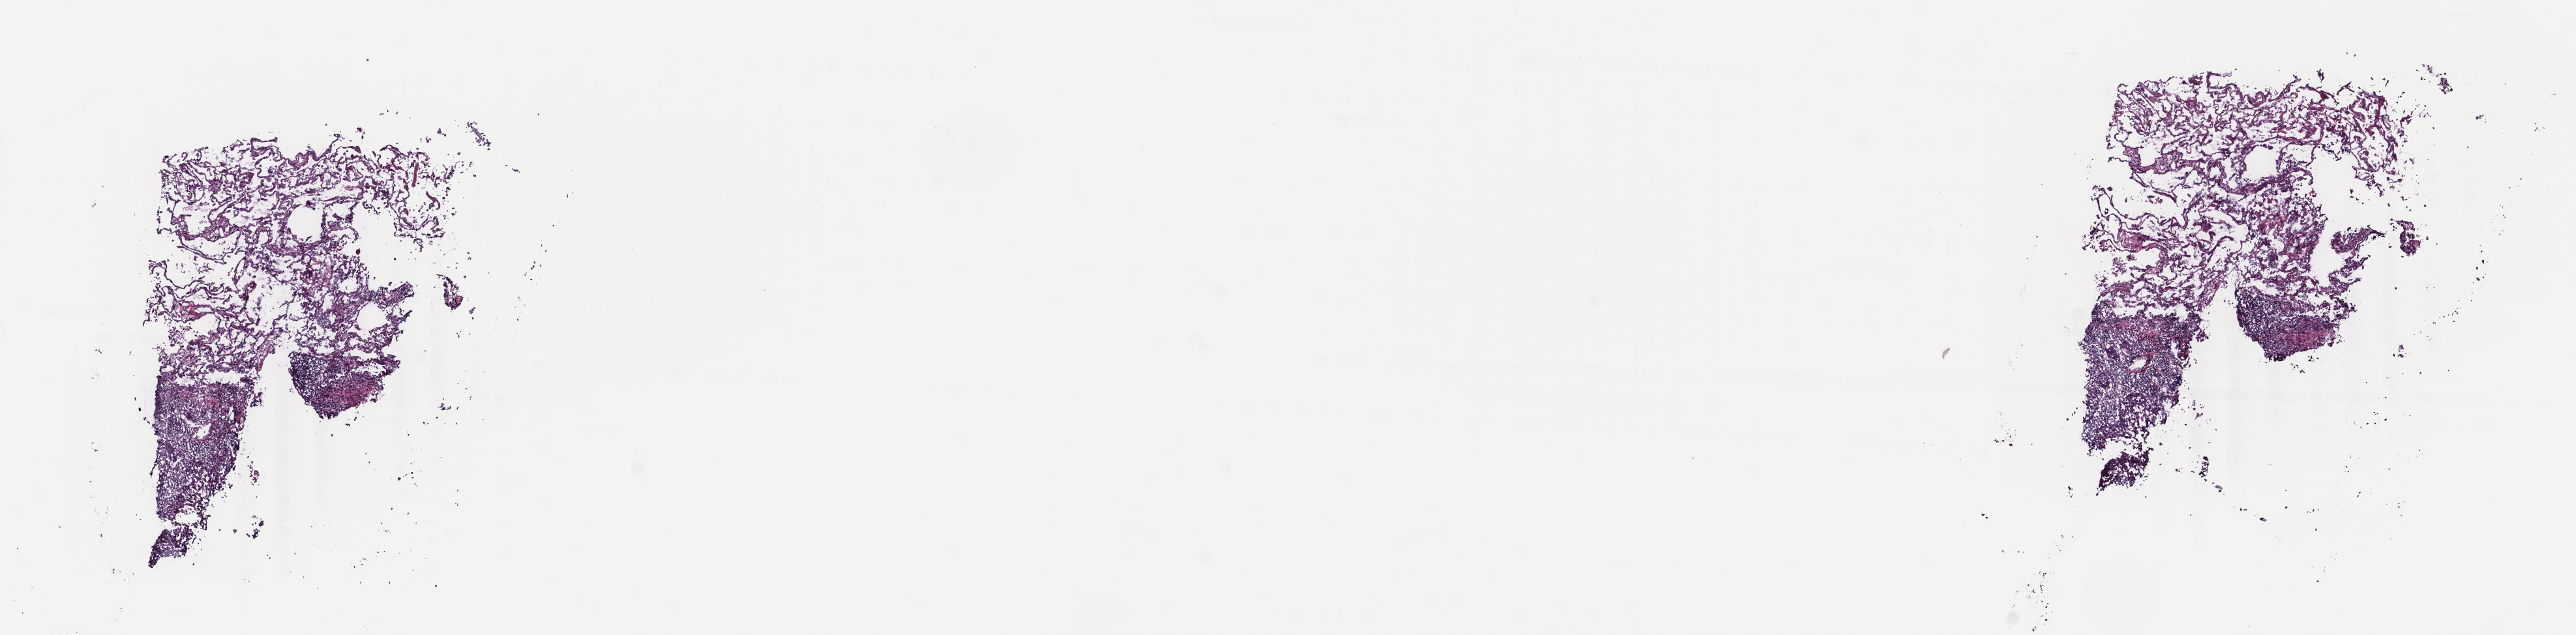
Hematoxylin and eosin (H&E) stained whole-slide image, whole scanned area (about 15.7 x 3.9 mm, acquisition: 40x scan) shown as a low-resolution overview, frozen section from the top of the tissue portion, lung, primary tumour sample. Male, age 73 years at initial diagnosis. Slide review estimates, as recorded: tumour cells 15%, tumour nuclei 95%, normal cells 70%, stromal cells 15%, necrosis 0%. Infiltration values recorded for this section: lymphocyte infiltration 6%, monocyte infiltration 4%, neutrophil infiltration 1%.
• laterality: right
• AJCC pathologic stage: IIA (7th edition)
• pathologic diagnosis: Squamous cell carcinoma, NOS (upper lobe, lung)